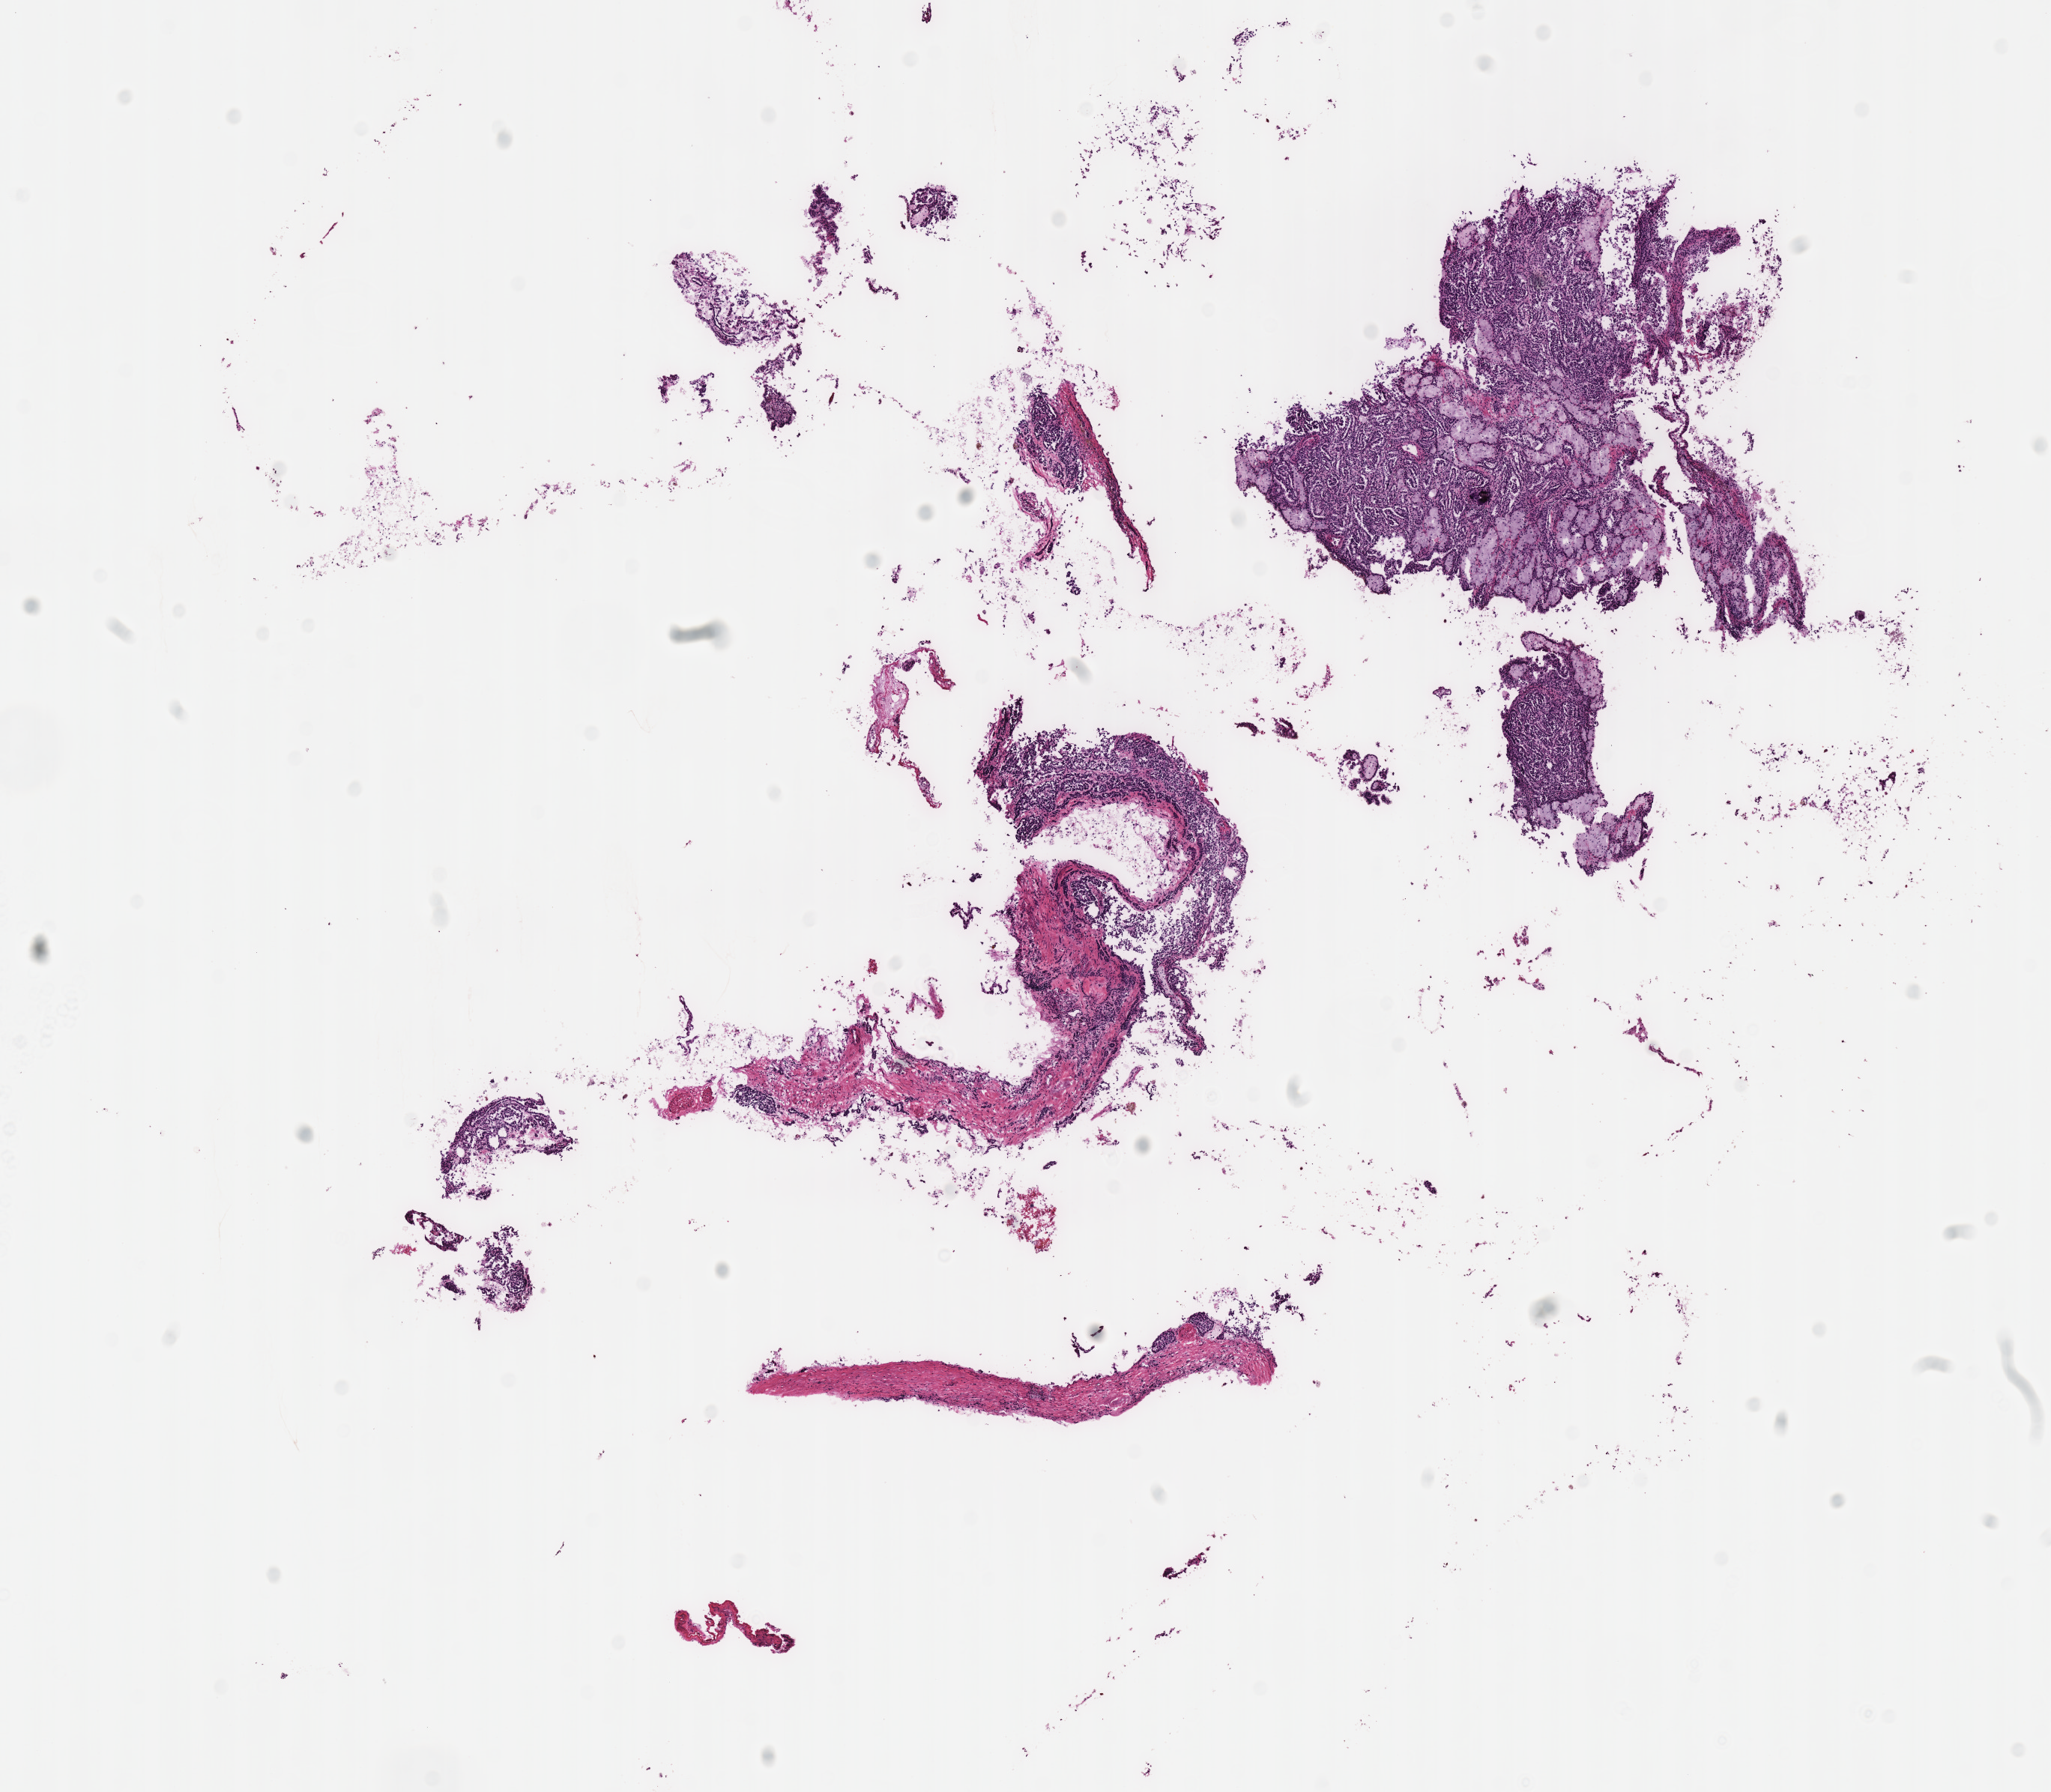
Whole-slide histology image, H&E-stained — shown as a low-resolution overview of the whole scanned area (about 10.8 x 9.4 mm, from a 40x scan), frozen section, kidney, primary tumour sample. Male patient; age at initial diagnosis 53 years. Pathologist review of this section (percent, as recorded): tumour cells 80%, tumour nuclei 80%, normal cells 0%, stromal cells 20%, necrosis 0%. Infiltration values recorded for this section: lymphocyte infiltration 0%, monocyte infiltration 15%, neutrophil infiltration 0%.
• AJCC pathologic stage: I (5th edition)
• laterality: left
• histologic diagnosis: Papillary adenocarcinoma, NOS